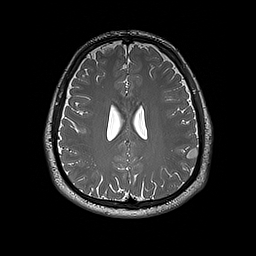
Brain MRI from a brain-tumour surgery series, one axial slice. Slice 75 of 192 in the series (ordered by position). 256 × 256 image matrix, field of view 250 × 250 mm. From the clinical record (not read from this slice): histopathology: Dysembryoplastic neuroepithelial tumor; WHO grade: 1.
Annotated regions visible in this slice (outlined manually by an expert reader):
- tumour: bounding box (x1, y1, x2, y2) in pixels: (187, 147, 199, 158)